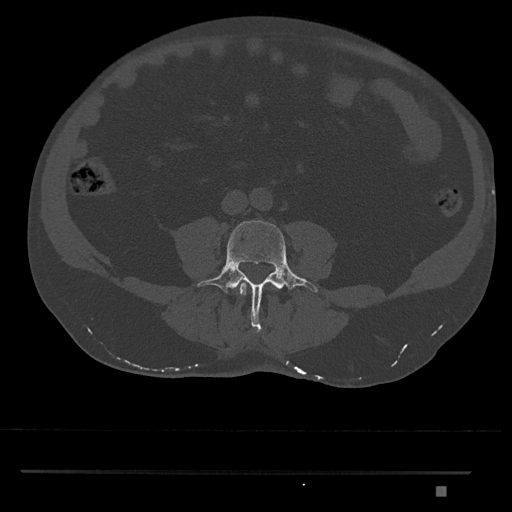
CT including the spine, one axial slice. Position 624 of 1134 along the scan axis. Reconstruction kernel Br40s/3. 120 kVp. Bone window (W 1800 / L 400 HU). 0.5 mm slice thickness. 512 × 512 image matrix. Patient: male, 65 years. From the clinical record (not read from this slice): primary cancer: prostate.
Structures marked on this image (semi-automatic segmentation, software-assisted and operator-edited):
- L3 vertebra: bounding box <239,282,278,296> (left, top, right, bottom; pixels)
- L4 vertebra: <197,220,318,333>